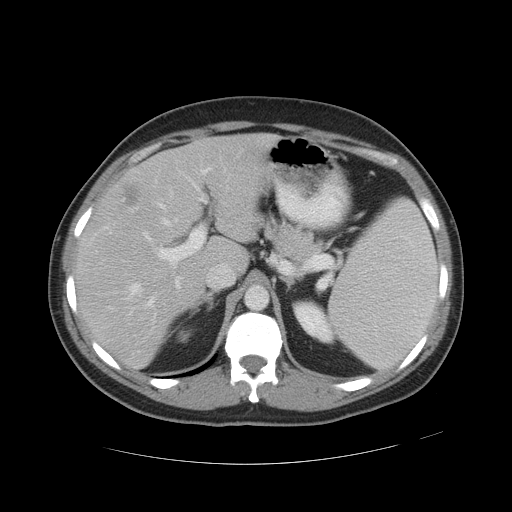
Contrast-enhanced abdominal CT, one axial slice. Reconstruction kernel STANDARD. Soft-tissue window (W 400 / L 40 HU). 512 × 512 image matrix, field of view 422 × 422 mm. Male patient, age 42 years. From the clinical record (not read from this slice): diagnosis: colorectal cancer liver metastases, imaged before liver resection; multiple liver metastases: yes.
Structures marked on this image (expert manual segmentation):
- hepatic veins: bounding box [x1, y1, x2, y2] px = [128, 167, 226, 307]
- liver: [77, 135, 268, 366]
- planned liver remnant (the part of the liver to remain after resection): [77, 135, 267, 366]
- portal vein (with intrahepatic branches): [147, 186, 228, 307]
- liver metastasis: [122, 186, 139, 209]